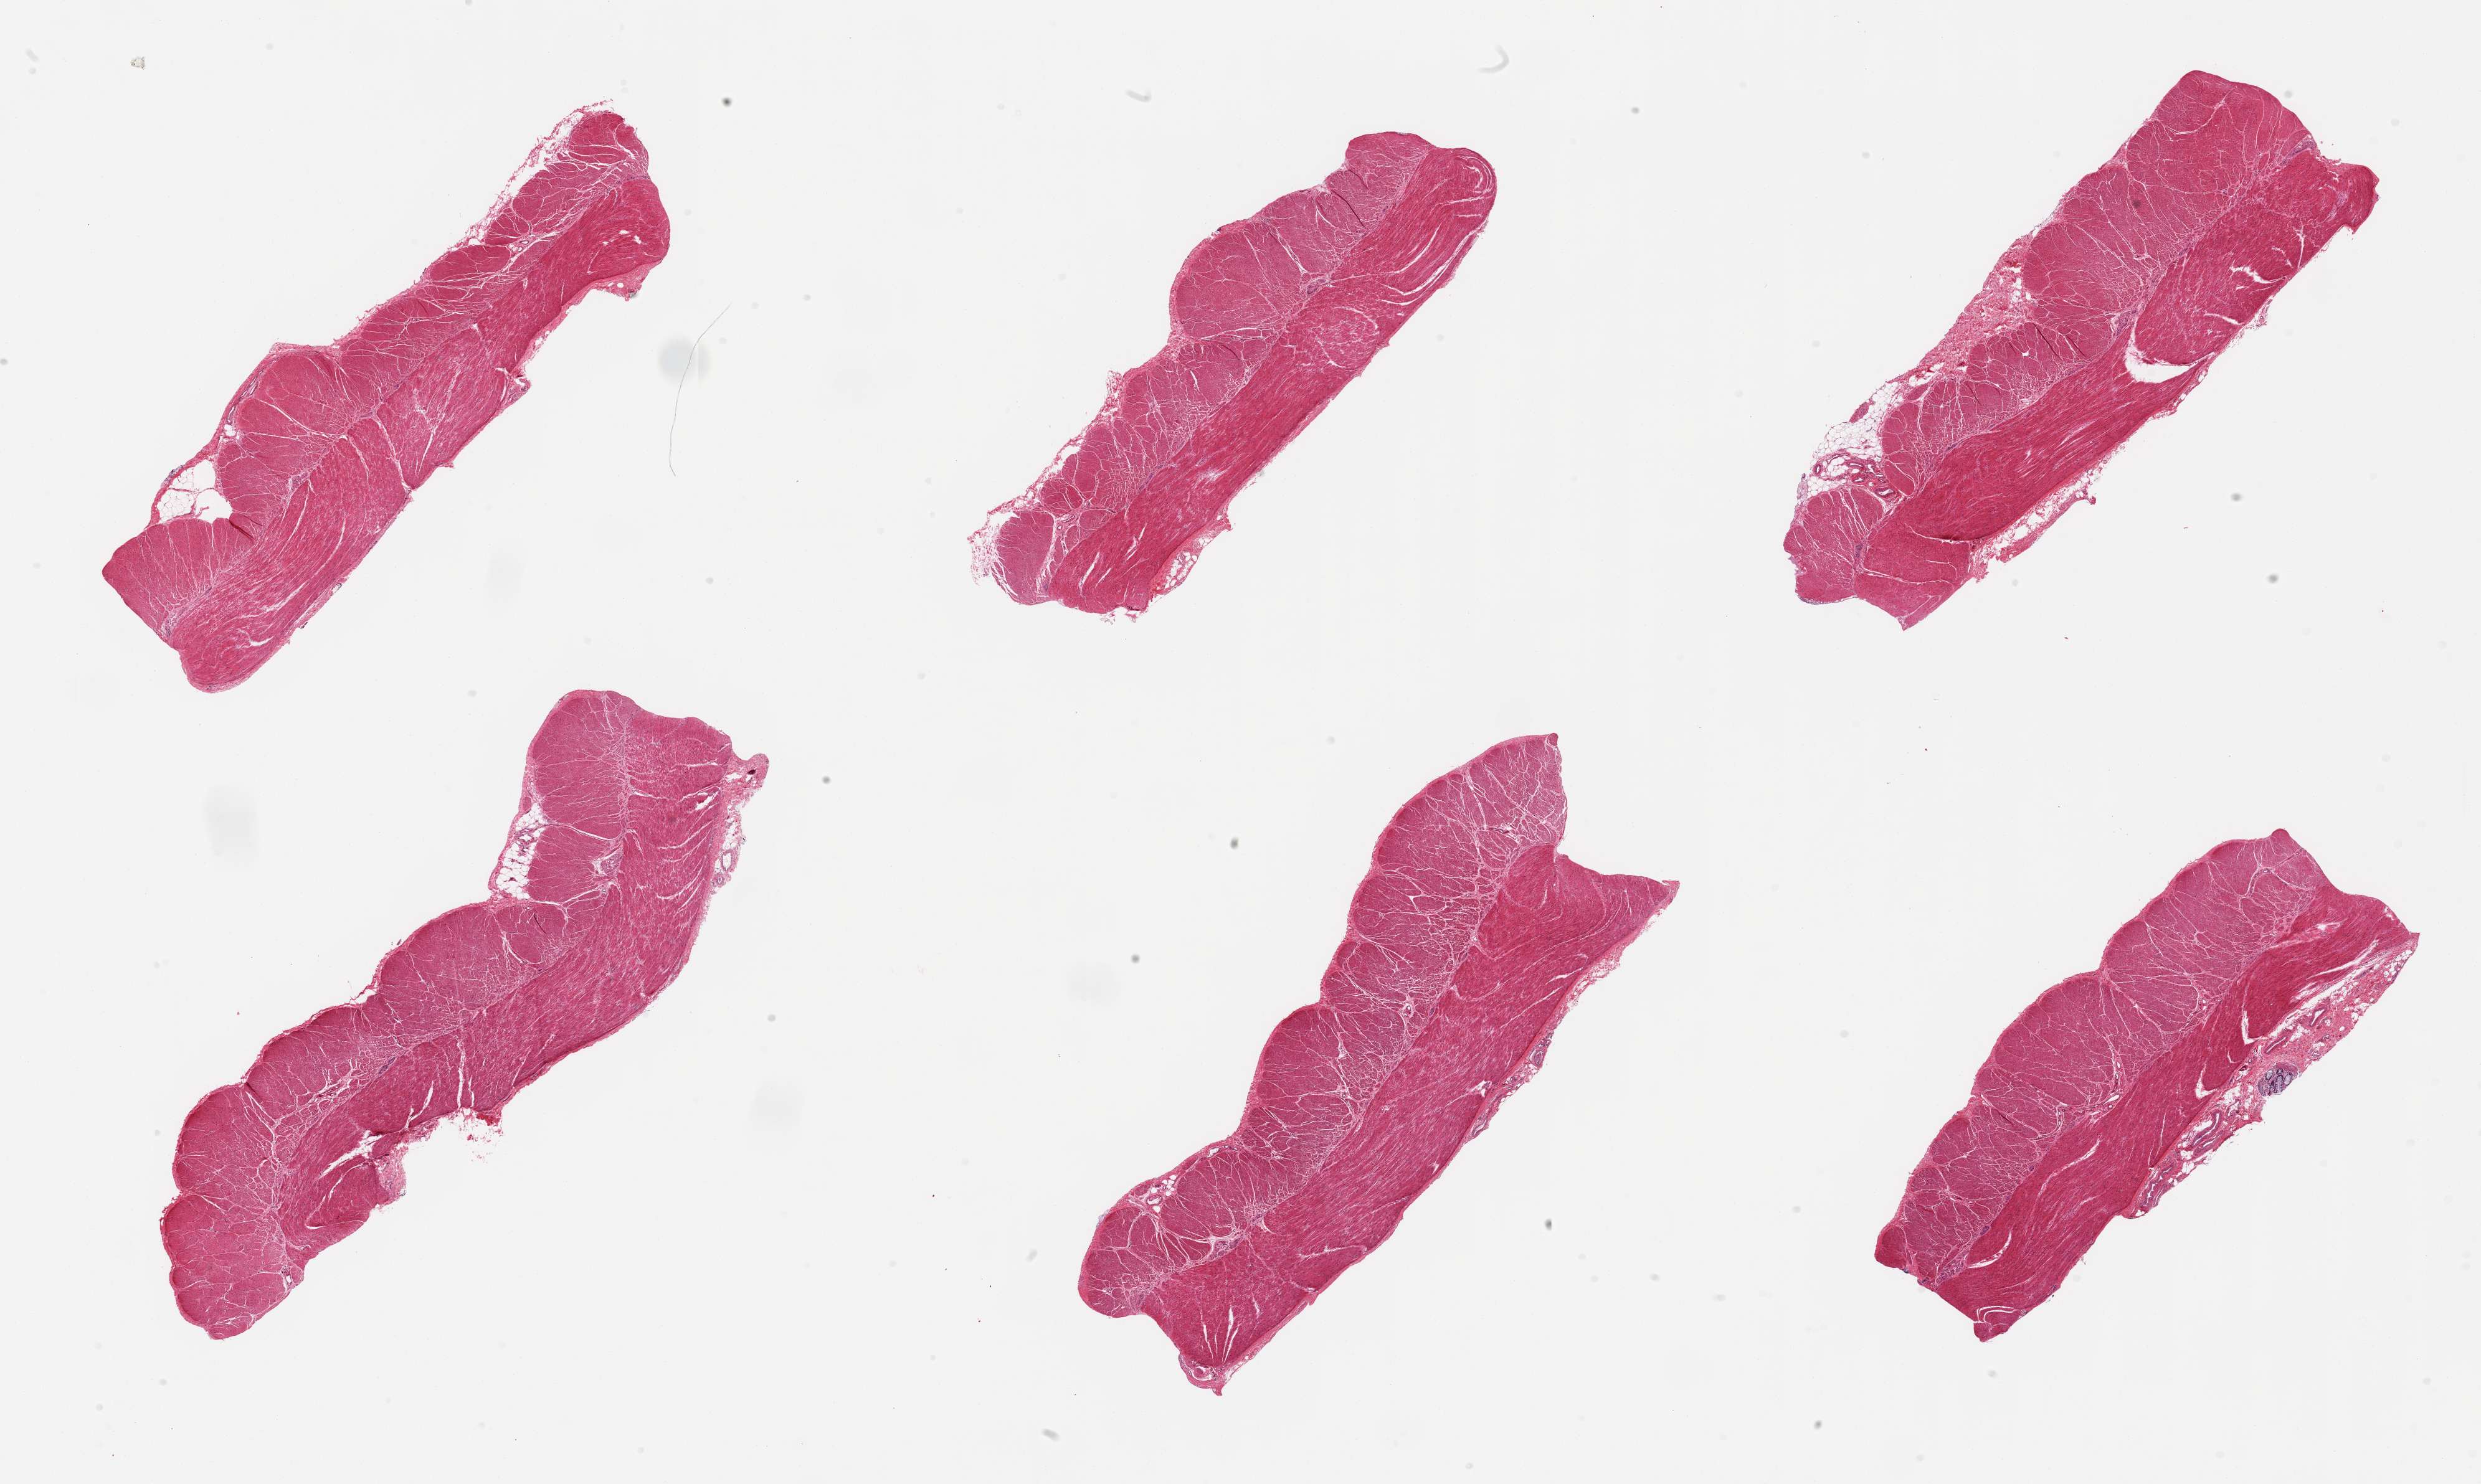
Haematoxylin and eosin whole-slide image, brightfield, whole scanned area (about 31.5 x 18.8 mm, from a 20x scan) shown as a low-resolution overview. PAXgene-fixed, paraffin-embedded tissue. Target tissue: sigmoid colon. Tissue donor sample. Donor: male.
* pathologist's review note for this sample: 6 pieces, confirmed target muscularis; Minute (<0.5mm) focus 'contaminant' mucosa